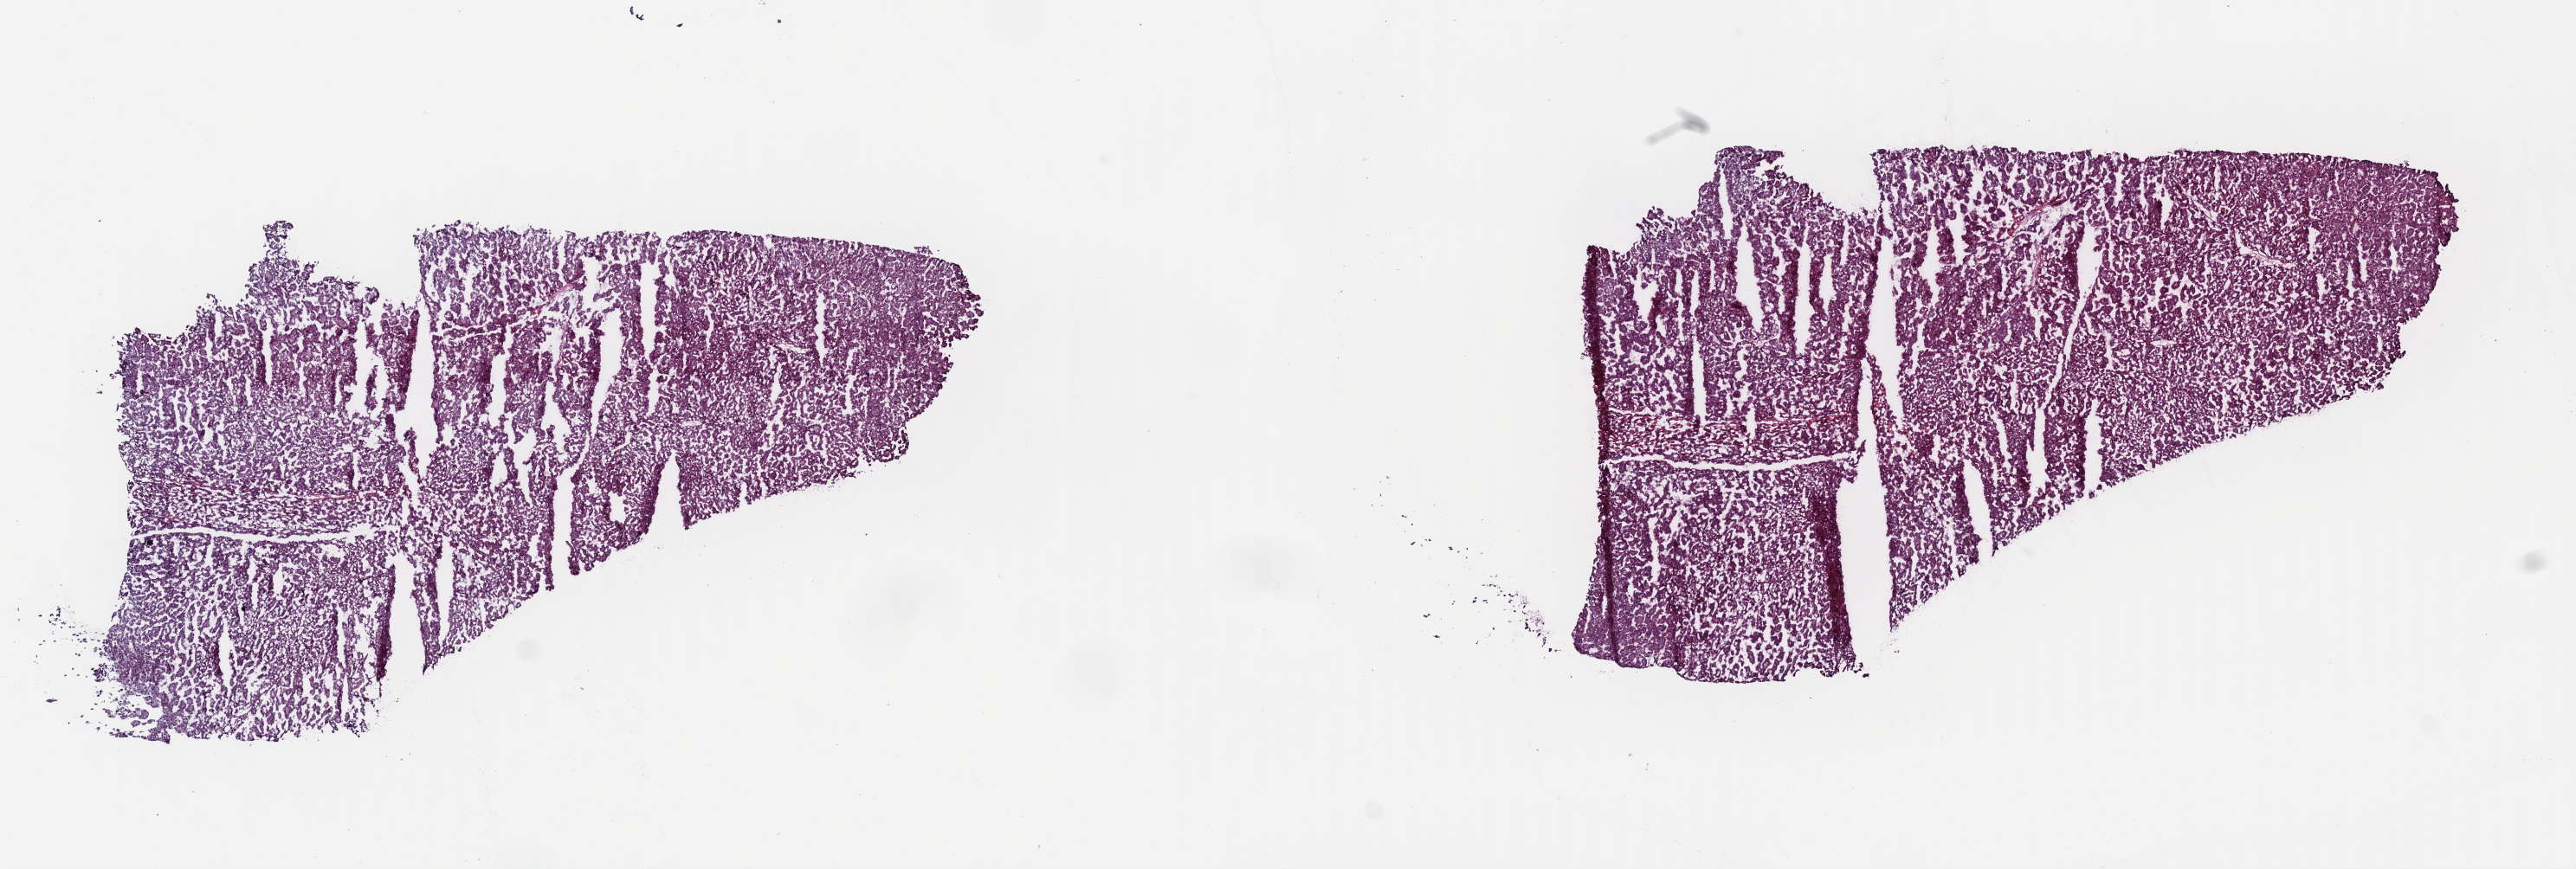
H&E-stained whole-slide image — whole scanned area (about 23.4 x 7.9 mm) shown as a low-resolution overview. Frozen section from the top of the tissue portion. Sample: primary tumour, liver. Male patient; age at initial diagnosis 71 years. Histologic grade: G1 (well differentiated). Composition of this section per pathologist review: tumour cells 100%, tumour nuclei 95%, normal cells 0%, stromal cells 0%, necrosis 0%. Inflammatory infiltration, as recorded: lymphocyte infiltration 0%, monocyte infiltration 0%, neutrophil infiltration 0%.
• histologic diagnosis: Hepatocellular carcinoma, NOS
• AJCC pathologic stage: IIIA